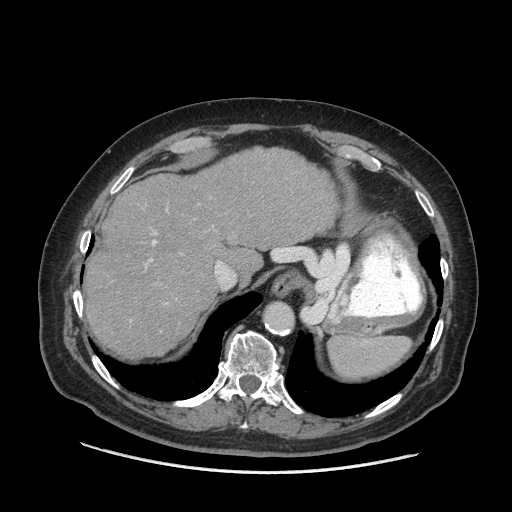
Contrast-enhanced abdominal CT (liver protocol), one axial slice. Slice 54 of 77 in the series (ordered by position). Reconstruction kernel STANDARD. 140 kVp. Soft-tissue window (W 400 / L 40 HU). 2.5 mm slice thickness. 512 × 512 image matrix. From the clinical record (not read from this slice): diagnosis: hepatocellular carcinoma (patient treated with transarterial chemoembolisation; whether this scan precedes or follows treatment is not stated here); TNM stage (as recorded): Stage-I; Child-Pugh class: A; tumour differentiation: well differentiated; tumour nodularity: uninodular.
Structures marked on this image (semi-automatic segmentation, software-assisted and operator-edited):
- abdominal aorta: bounding box <265,303,292,330> (left, top, right, bottom; pixels)
- liver parenchyma outside the tumour (the mass and vessels are separate outlines, so this box may not span the whole liver): <84,148,338,358>
- liver vessels: <150,232,157,261>